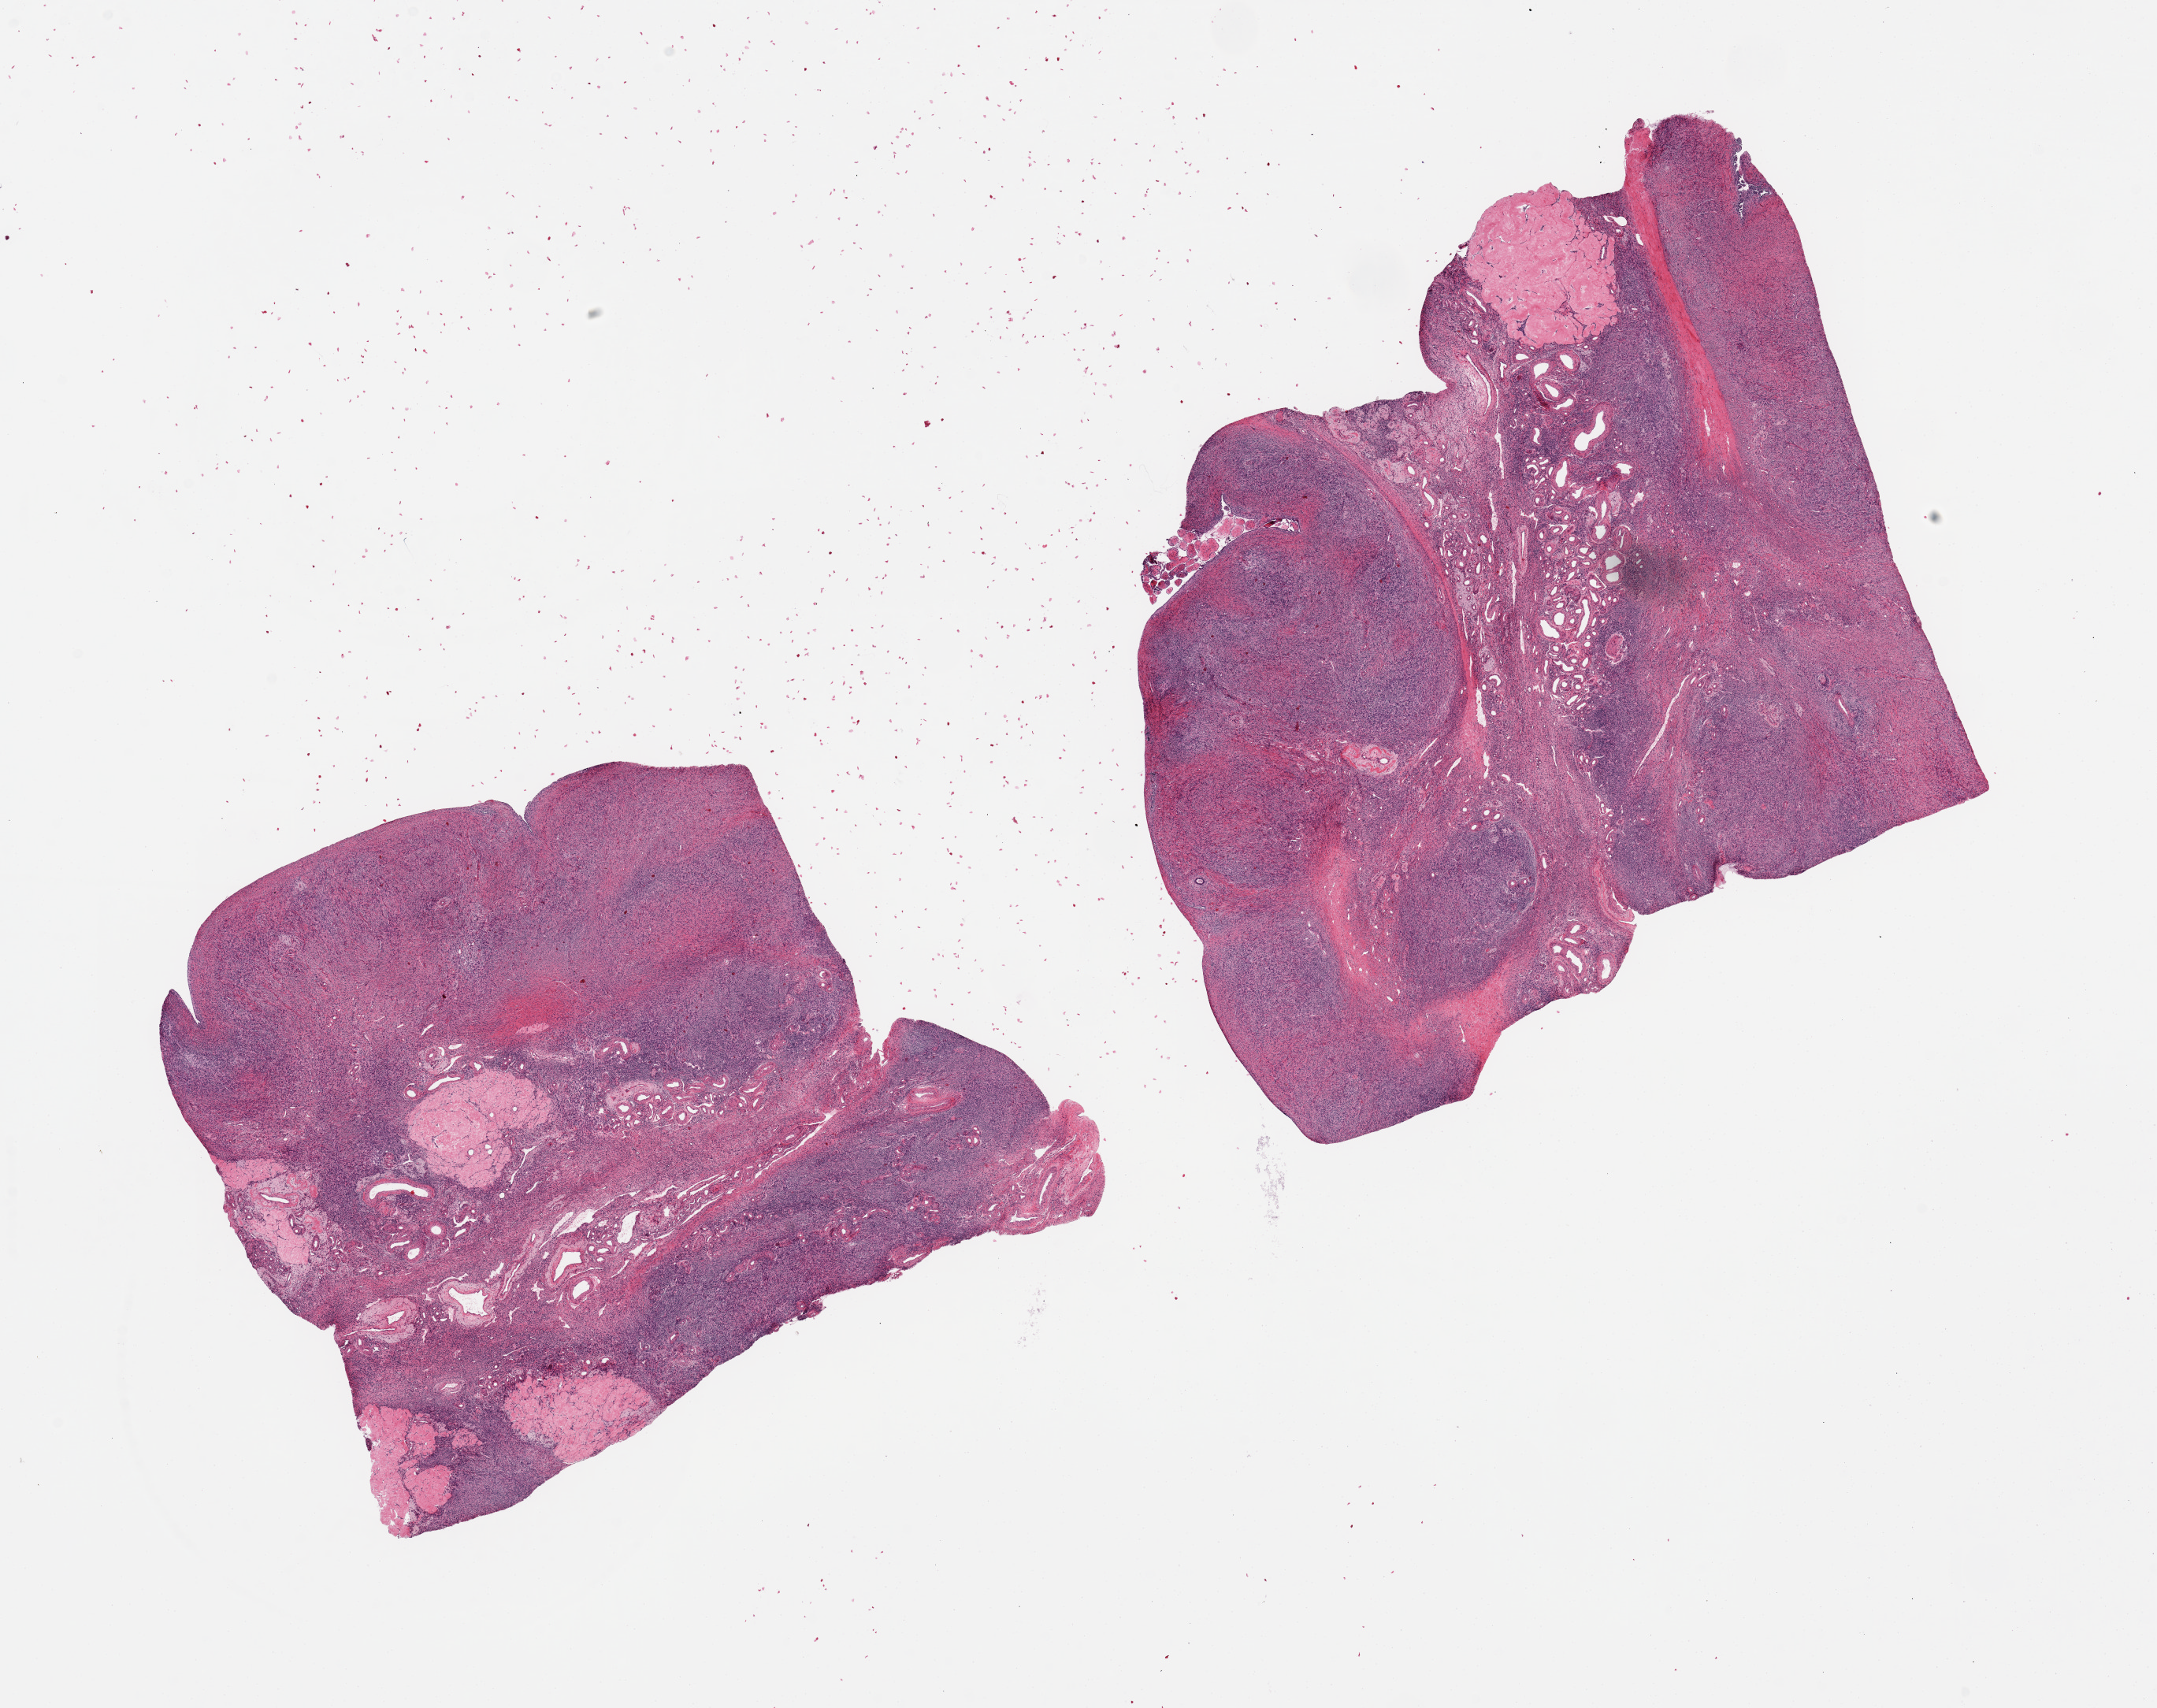
H&E whole-slide image, brightfield, low-resolution overview of the scanned area, about 21.7 x 17.1 mm; PAXgene-fixed paraffin-embedded (PFPE) section; section of ovary (target tissue); donor tissue sample. Donor sex: female.
Review note (as recorded): 2 pieces, 8.5x7 & 8.5x8mm; tiny (early) serous cystadenofibroma on surface of 1 piece.